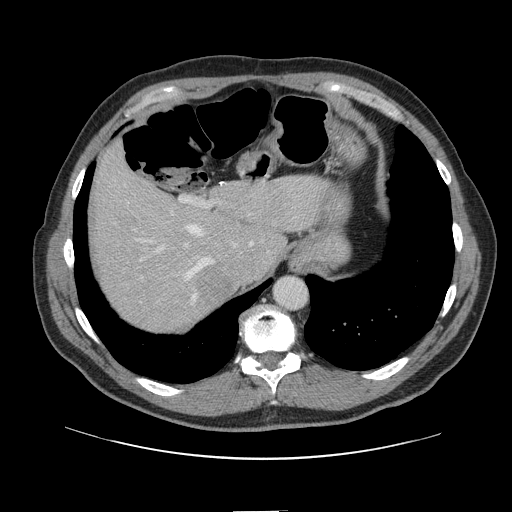
Contrast-enhanced abdominal CT, one axial slice. 120 kVp. Intravenous contrast given. Soft-tissue window (W 400 / L 40 HU). 2.5 mm slice thickness. 512 × 512 image matrix, field of view 412 × 412 mm. Male patient, age 66 years. Case-level facts recorded for this patient, not image findings: diagnosis: colorectal cancer liver metastases, imaged before liver resection; multiple liver metastases: no; largest metastasis: 3.5 cm; disease in both lobes: no.
Structures marked on this image (expert manual segmentation):
- hepatic veins: bounding box (x1, y1, x2, y2) in pixels: (135, 214, 251, 304)
- liver: (93, 148, 323, 332)
- planned liver remnant (the part of the liver to remain after resection): (93, 148, 323, 305)
- portal vein (with intrahepatic branches): (133, 196, 221, 280)
- liver metastasis: (196, 262, 229, 306)